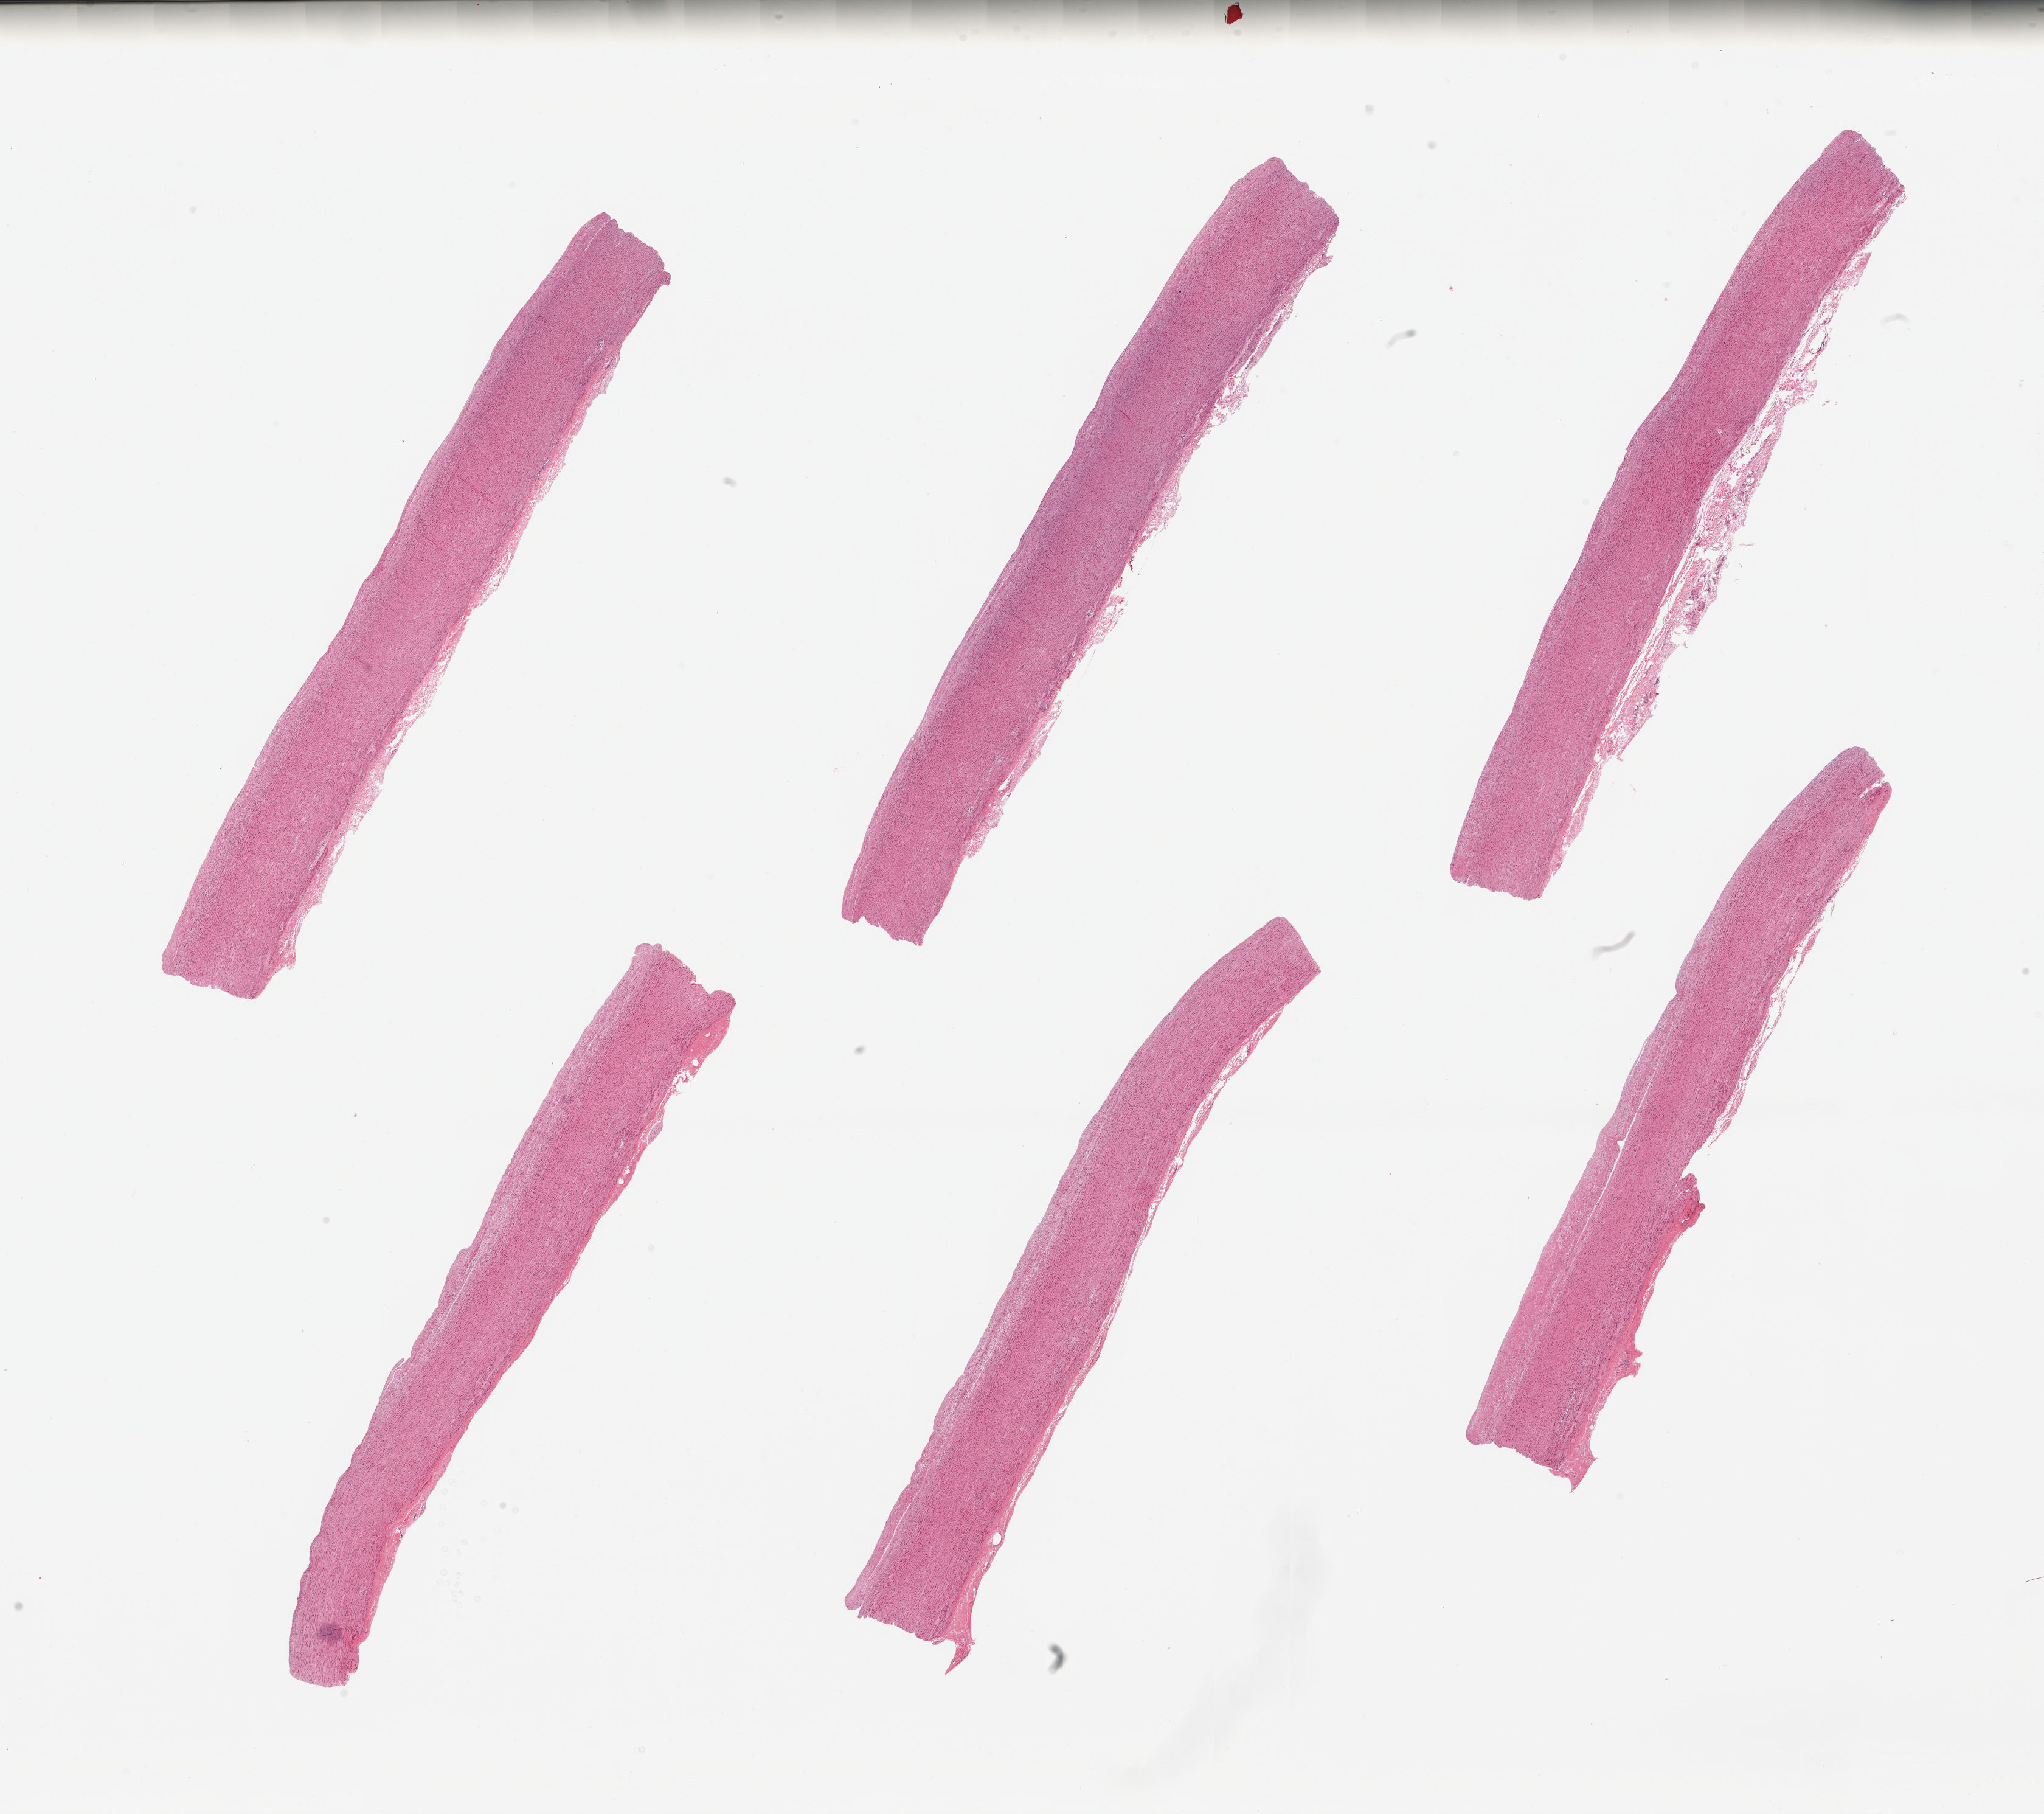
Digitized haematoxylin and eosin-stained section — shown as a low-resolution overview of the whole scanned area (about 26.6 x 23.6 mm, acquisition: 20x scan), PAXgene-fixed, paraffin-embedded tissue, target tissue: aorta, tissue donor sample. Donor sex: male.
• pathologist's review note for this sample: 6 pieces; mild atherosclerosis